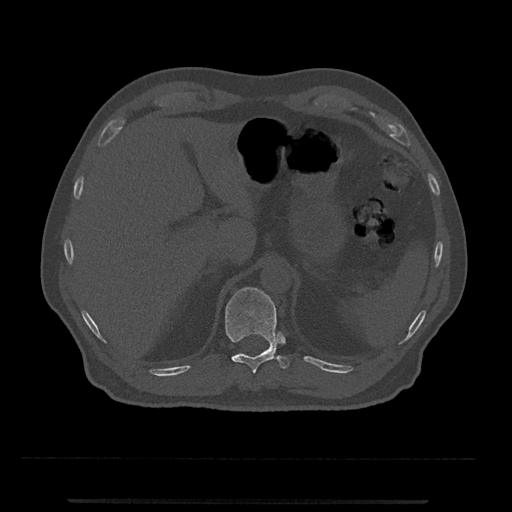
CT including the spine, one axial slice; position 460 of 797 along the scan axis; reconstruction kernel Br40s/3; 120 kVp; bone window (W 1800 / L 400 HU); 0.5 mm slice thickness; 512 × 512 image matrix, field of view 419 × 419 mm. Patient: male, 63 years. From the clinical record (not read from this slice): primary cancer: prostate.
Structures marked on this image (semi-automatically segmented with operator editing):
- T11 vertebra: bounding box <225,287,290,374> (left, top, right, bottom; pixels)